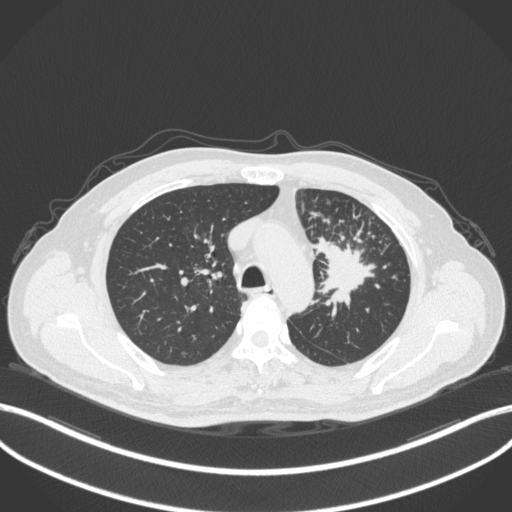
Chest CT, one axial slice; position 261 of 386 along the scan axis; reconstruction kernel B31f; 120 kVp; lung window (W 1500 / L -600 HU); 1 mm slice thickness; 512 × 512 image matrix, field of view 400 × 400 mm. Patient: male, 69 years. From the clinical record (not read from this slice): clinical TNM (as recorded): T2a N2 M0.
Annotated regions visible in this slice (rectangle marked by the reading radiologist):
- lung tumour (recorded histology: adenocarcinoma): box from (x=316, y=236) to (x=385, y=309) px